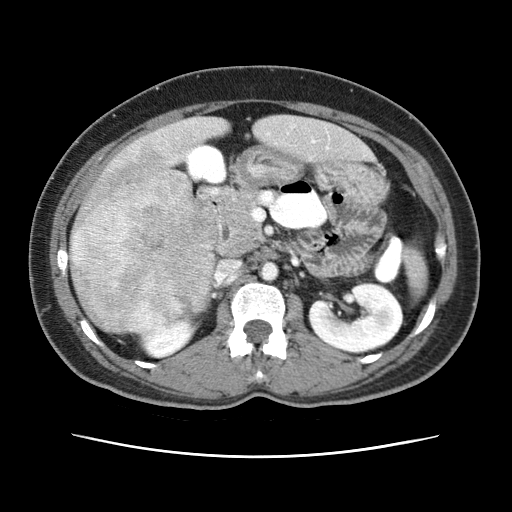
Contrast-enhanced abdominal CT (liver protocol), one axial slice. Slice 18 of 79 in the series (ordered by position). Reconstruction kernel STANDARD. 120 kVp. Soft-tissue window (W 400 / L 40 HU). 2.5 mm slice thickness. 512 × 512 image matrix, field of view 340 × 340 mm. Case-level facts recorded for this patient, not image findings: diagnosis: hepatocellular carcinoma (patient treated with transarterial chemoembolisation; whether this scan precedes or follows treatment is not stated here); TNM stage (as recorded): Stage-I; Child-Pugh class: A; tumour nodularity: uninodular.
Structures marked on this image (semi-automatically segmented with operator editing):
- abdominal aorta: bounding box (x1, y1, x2, y2) in pixels: (260, 261, 278, 279)
- liver parenchyma outside the tumour (the mass and vessels are separate outlines, so this box may not span the whole liver): (70, 115, 370, 332)
- mass: (70, 145, 218, 334)
- liver vessels: (312, 140, 328, 149)